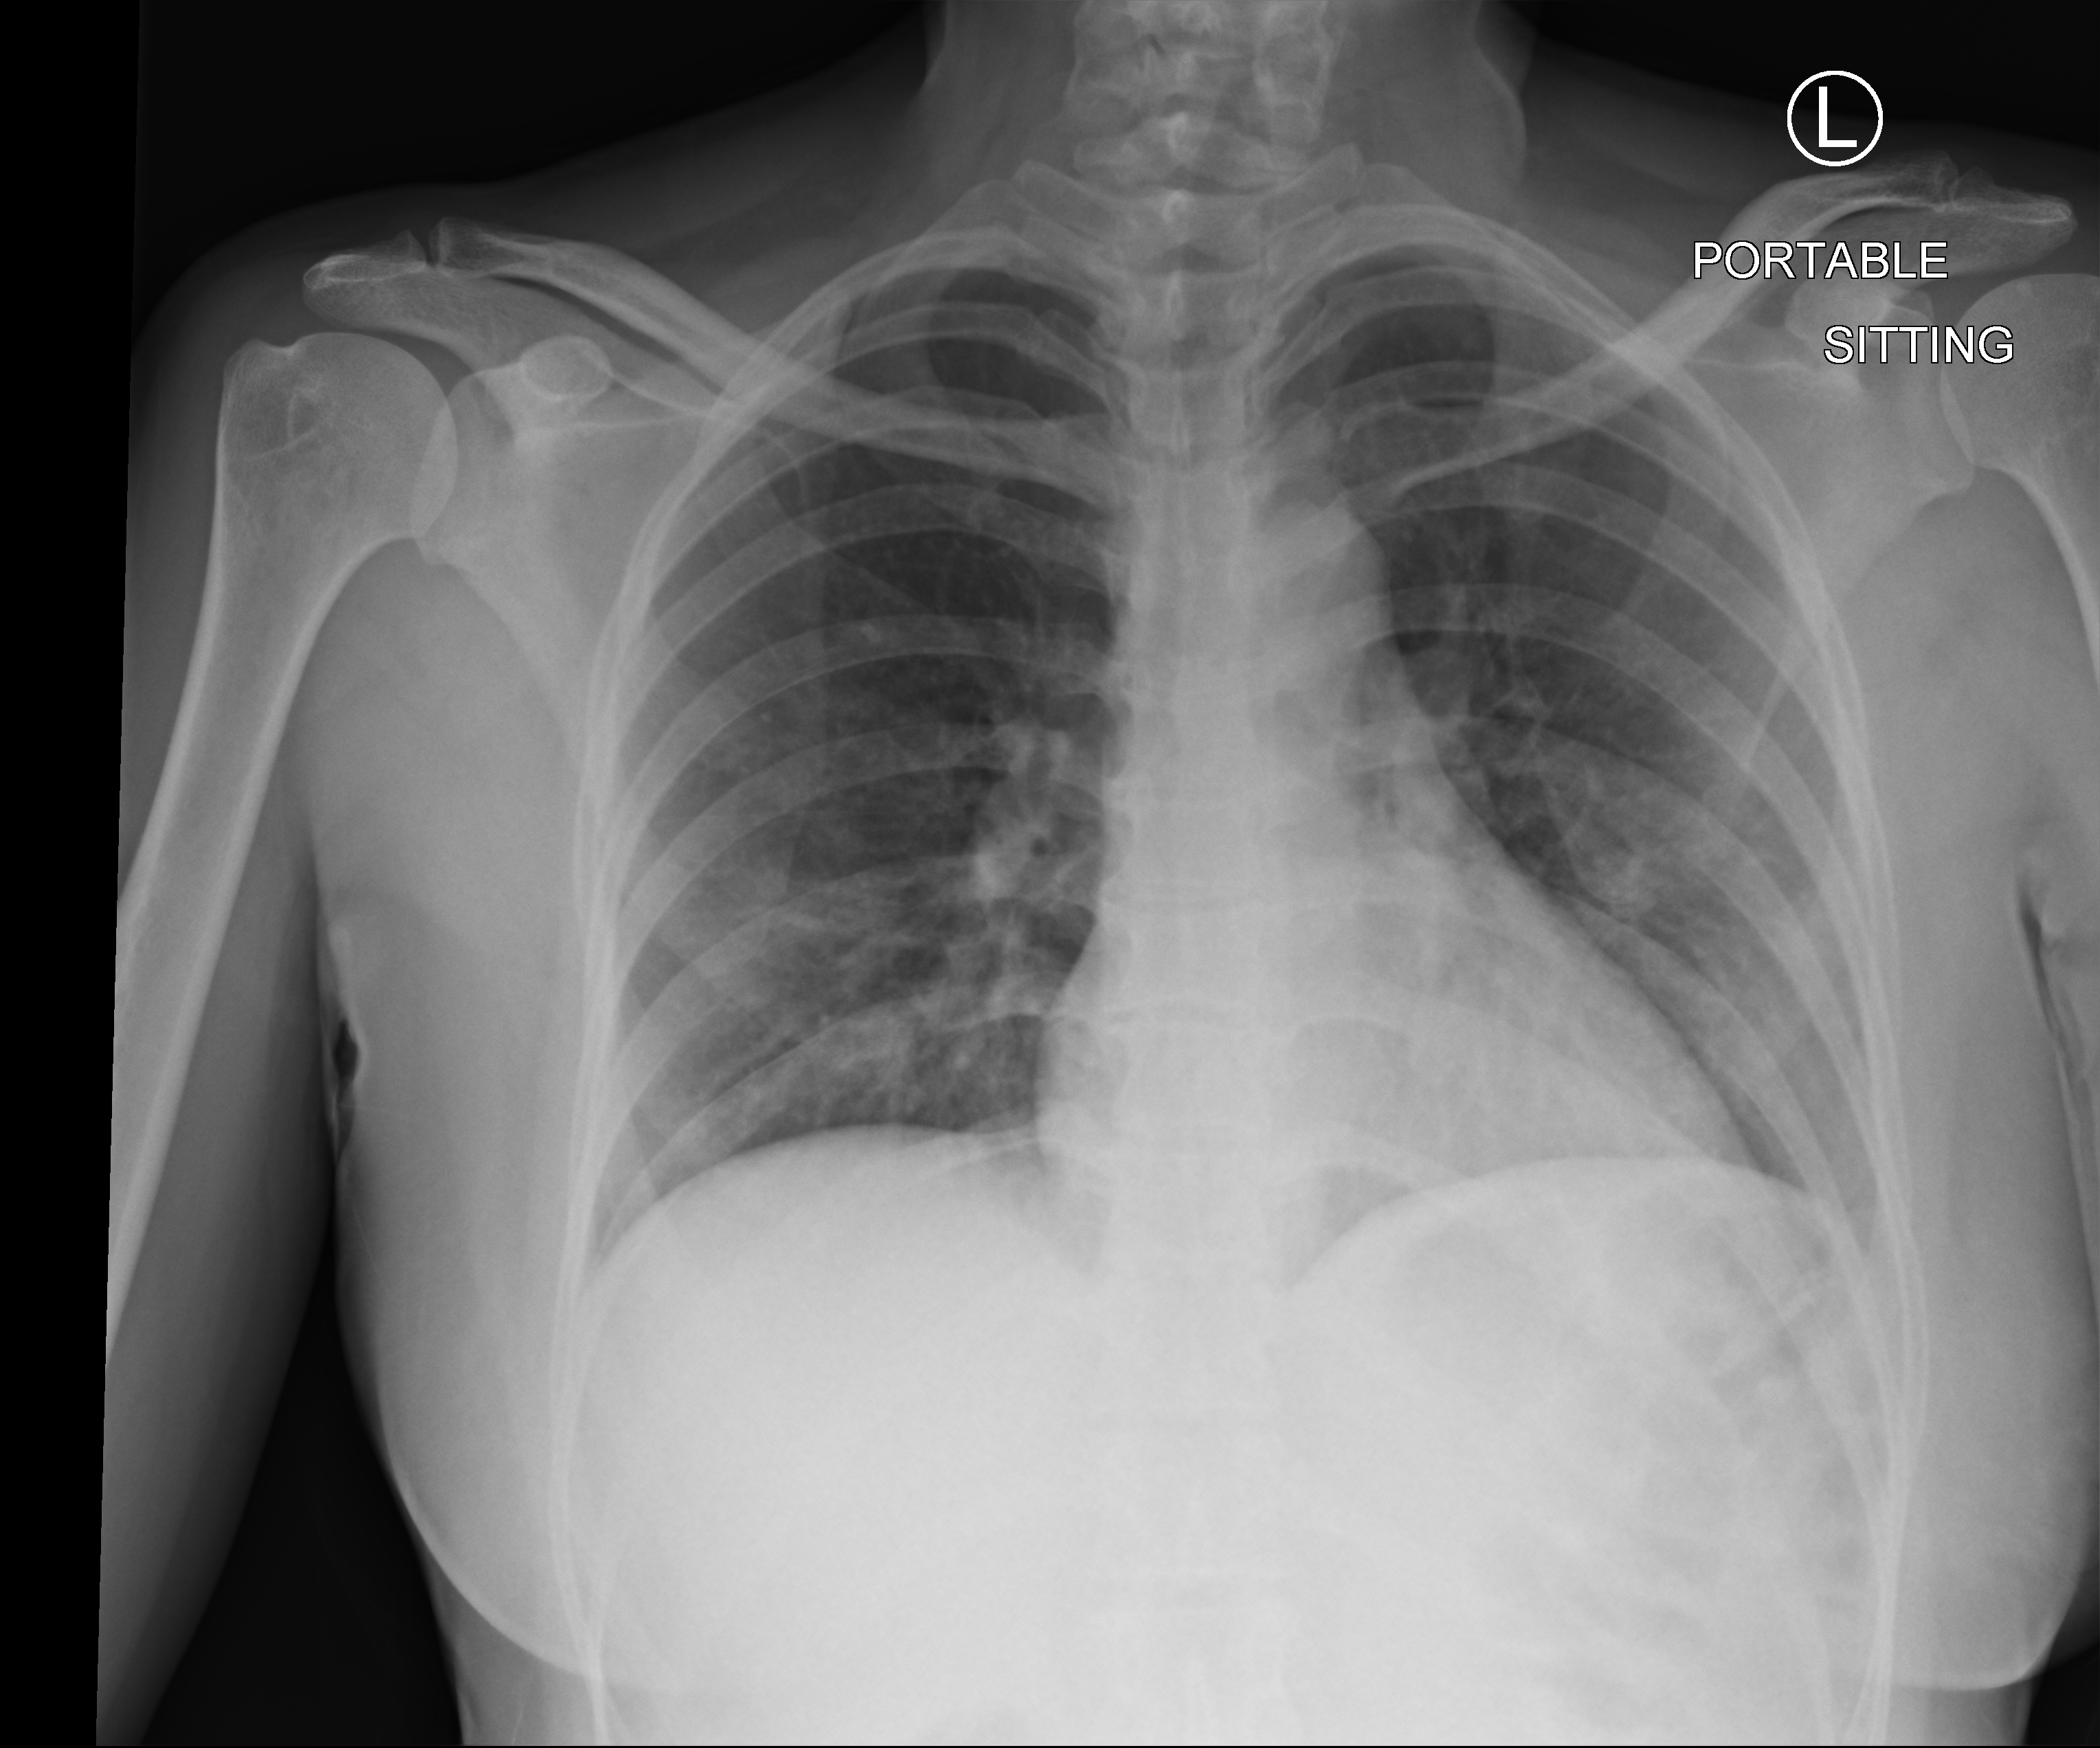
Chest X-ray (portable); anteroposterior (AP) projection. Female patient hospitalised with COVID-19, age 18–59 years.
Hospital-stay facts (about this admission, not read from this image; timing relative to this image not recorded): diabetes (admission record): no; other chronic lung disease (admission record): no.